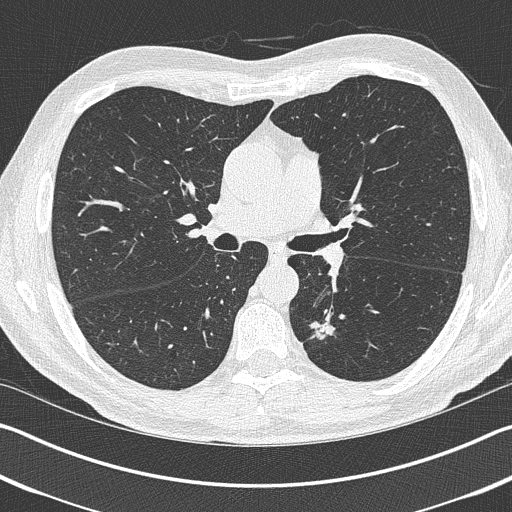
Chest CT (low-dose screening protocol), one axial image. First (baseline) screen. Lung window (W 1500 / L -600 HU). 1 mm slice thickness. Lung (sharp) reconstruction kernel (B50f). 512 × 512 image matrix, field of view 340 × 340 mm. Male participant, aged 69 years at enrolment. Current smoker at enrolment.
Expert-annotated lung lesion, bounding box <301,309,356,360> (left, top, right, bottom; pixels). Screening reader's record for this exam (one nodule recorded; not confirmed to be the boxed lesion): non-calcified nodule or mass ≥4 mm, left upper lobe, 19 × 19 mm, spiculated (stellate) margins, pre-existing on the prior screen: yes. Lung cancer was diagnosed 202 days after this screen: non-small cell carcinoma, left lower lobe, stage IIIA (AJCC 6th edition), 20 mm at pathology.